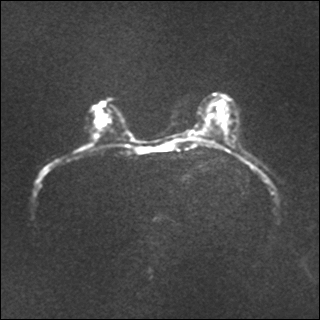
Breast MRI, one axial slice; slice 18 of 35 in the series (ordered by position); diffusion-weighted series; image 2 of 4 stored at this slice position (different b-values; order by instance number); 1.5 T; 4 mm slice thickness; 320 × 320 image matrix, field of view 320 × 320 mm. Female patient.
Outlined on this slice (manually delineated by an expert):
- tumour on diffusion-weighted imaging: box from (x=100, y=116) to (x=105, y=124) px